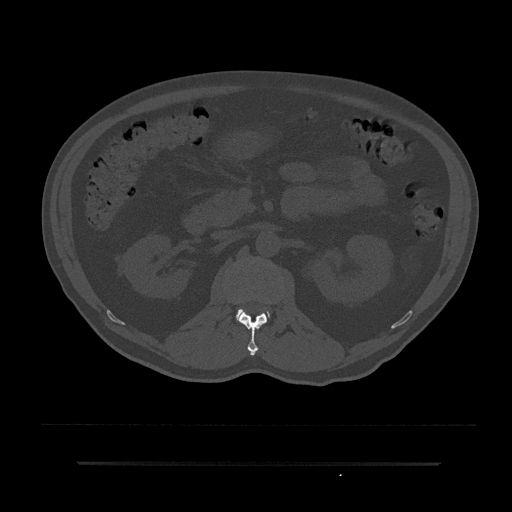
CT including the spine, one axial slice. Position 115 of 797 along the scan axis. Reconstruction kernel Br40s/3. 120 kVp. Bone window (W 1800 / L 400 HU). 0.5 mm slice thickness. 512 × 512 image matrix, field of view 464 × 464 mm. Patient: male, 59 years. Case-level facts recorded for this patient, not image findings: primary cancer: bile ducts.
Structures marked on this image (semi-automatic segmentation, software-assisted and operator-edited):
- L1 vertebra: box from (x=239, y=312) to (x=267, y=356) px
- L2 vertebra: (x=236, y=309)–(x=244, y=321)